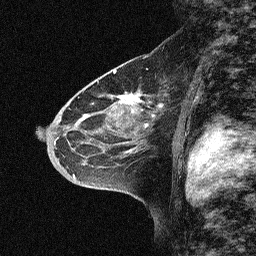
Breast MRI (dynamic contrast-enhanced), one sagittal slice; position 38 of 64 along the scan axis; dynamic contrast-enhanced study with each time point stored as its own series, time point 2 of 3 at this slice position (early post-contrast, ordered by acquisition time); 1.5 T; TE 4.5 ms, TR 11 ms; 256 × 256 image matrix, field of view 200 × 200 mm. Female patient, age 46 years. Case-level facts recorded for this patient, not image findings: setting: breast cancer imaged before/during neoadjuvant chemotherapy; receptor status: HER2-positive.
Structures marked on this image (semi-automatically segmented with operator editing):
- analysis volume of interest (the breast-tissue region the enhancement analysis was run in; not a lesion): bounding box [x1, y1, x2, y2] px = [46, 51, 180, 169]
- tumour enhancement mask (voxels above the 90 % enhancement threshold inside the analysis volume of interest): [120, 92, 148, 107]